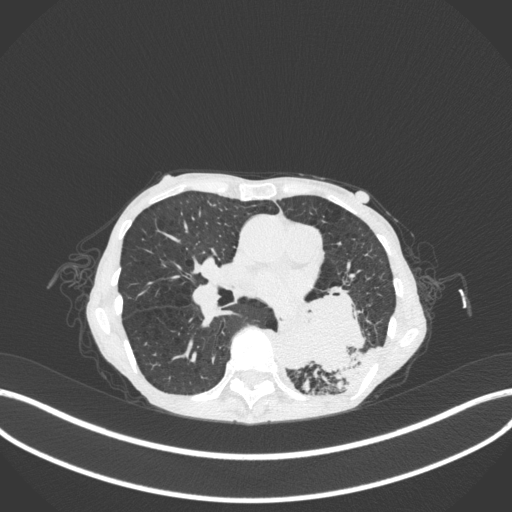
Chest CT, one axial slice. Position 137 of 347 along the scan axis. 120 kVp. Lung window (W 1500 / L -600 HU). 512 × 512 image matrix, field of view 400 × 400 mm. Female patient, age 70 years. From the clinical record (not read from this slice): clinical TNM (as recorded): T3 N0 M0; histopathological grade: G3.
Annotated regions visible in this slice (rectangle marked by the reading radiologist):
- lung tumour (recorded histology: small cell carcinoma): bounding box <283,278,367,372> (left, top, right, bottom; pixels)